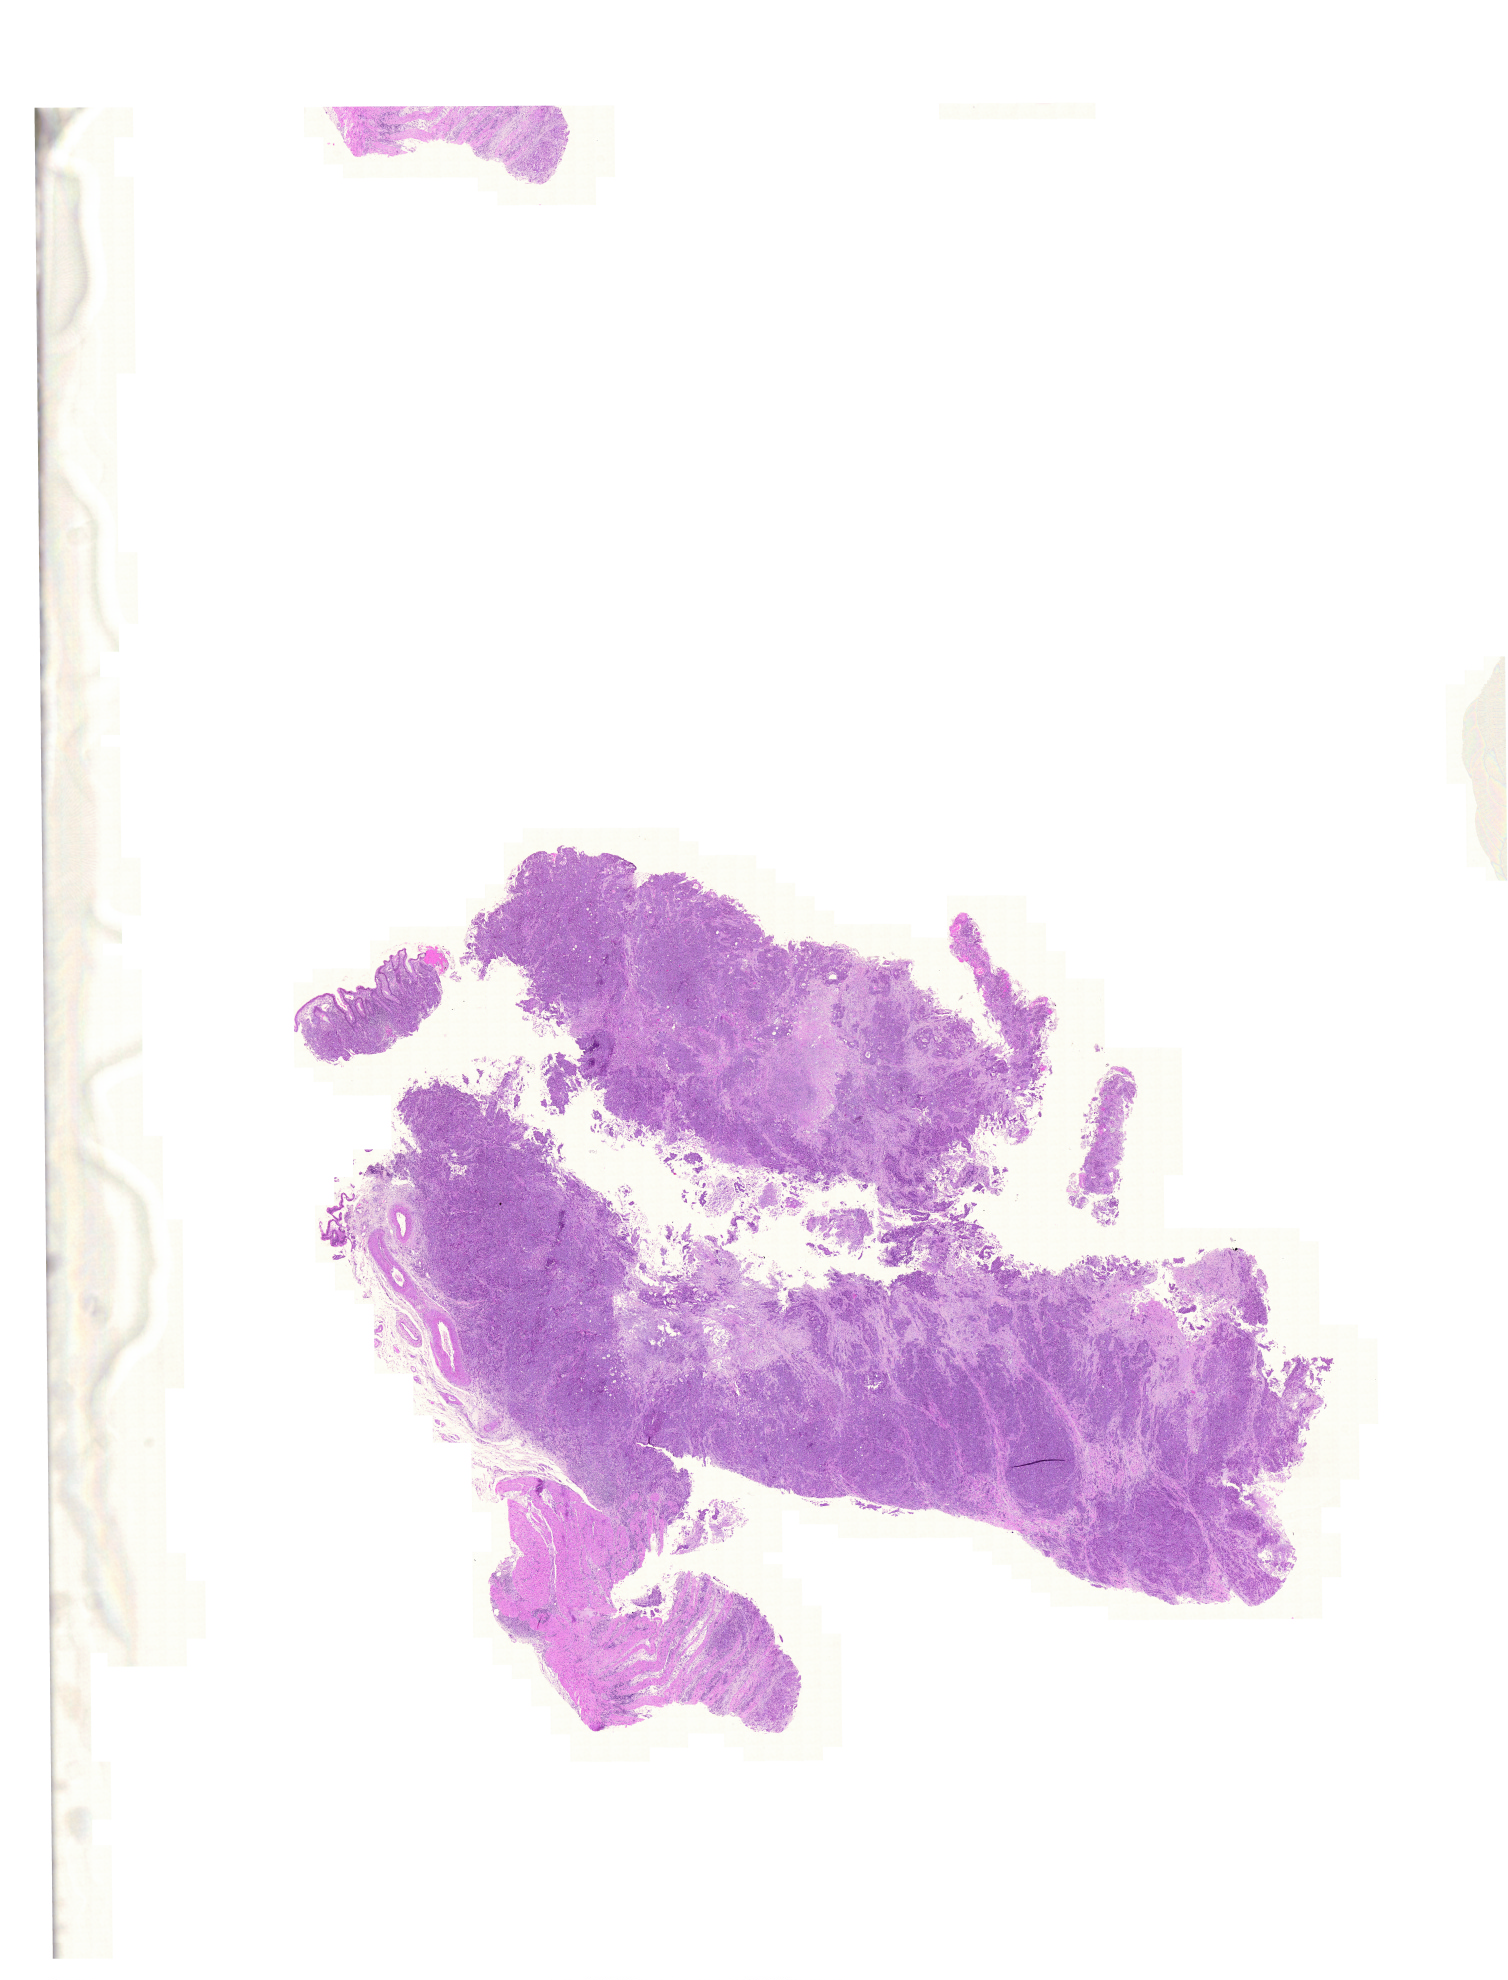
Digitized Hematoxylin and eosin (H&E) stained tissue section (whole slide), low-resolution overview of the scanned area, about 22.4 x 29.5 mm (slide scanned at 20x); formalin-fixed paraffin-embedded (FFPE) diagnostic section; colon, primary tumour sample. Female patient; age at initial diagnosis 80 years.
• pathologic diagnosis: Adenocarcinoma, NOS
• AJCC pathologic stage: III (5th edition)